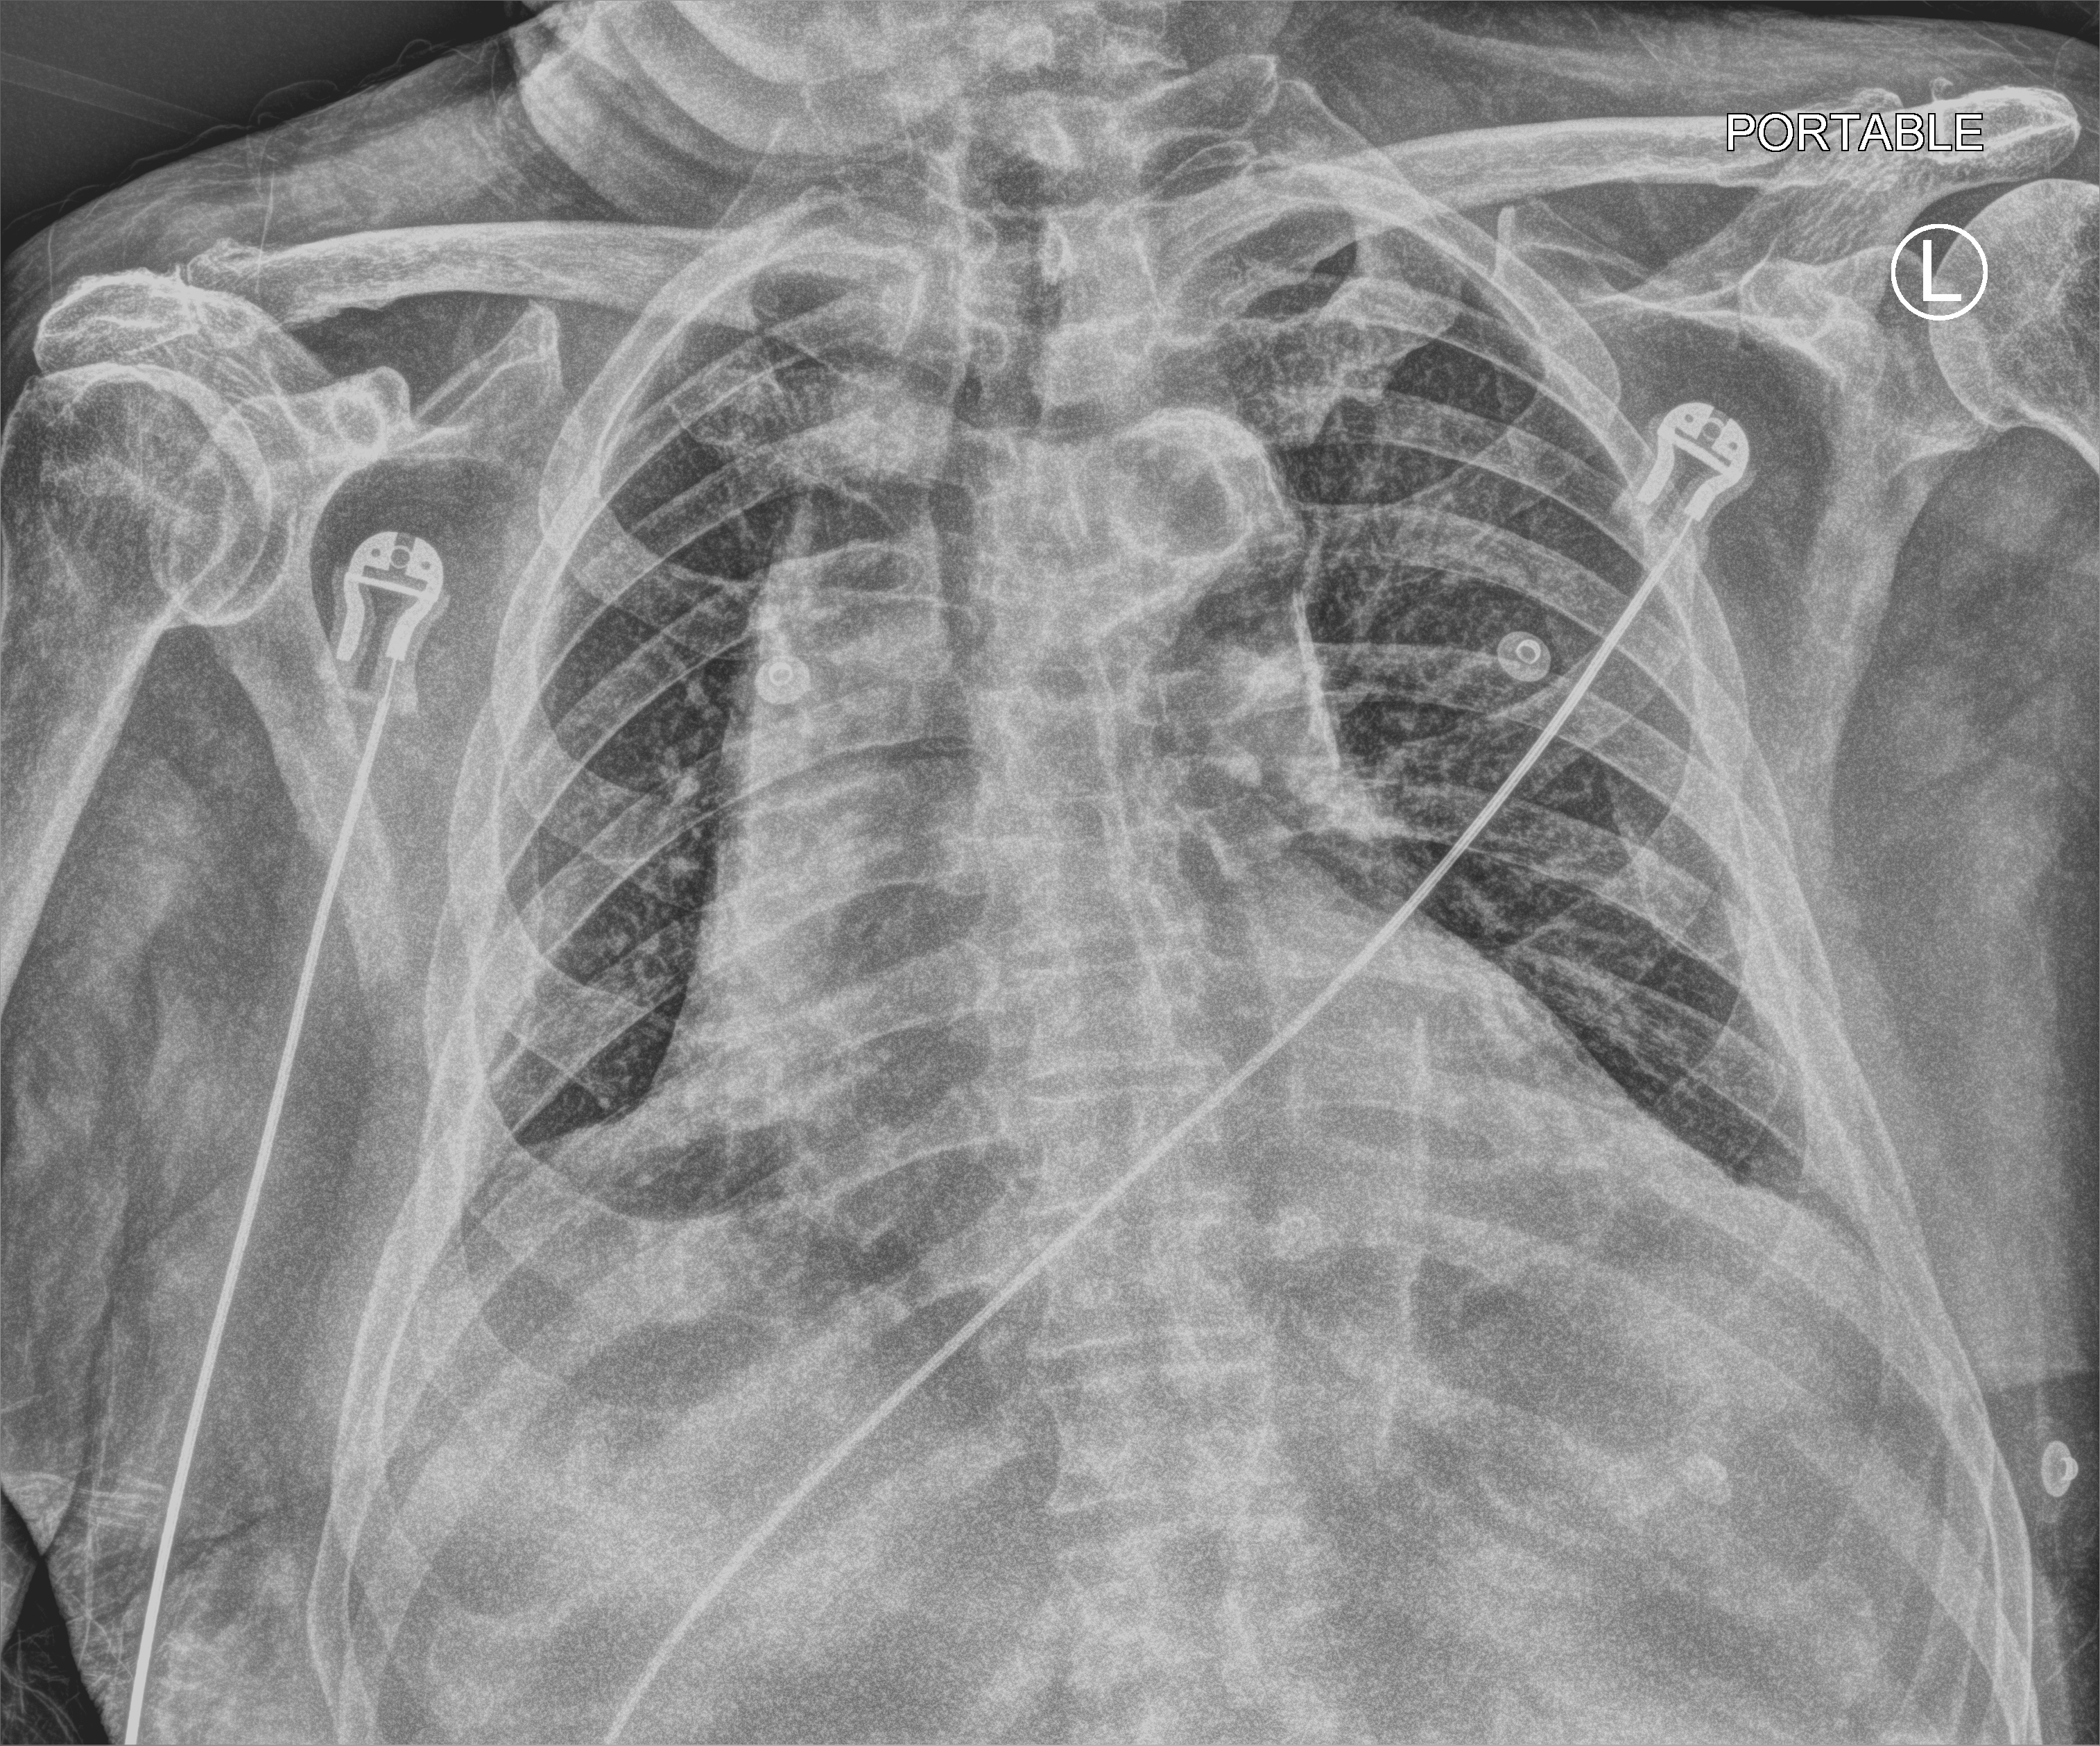
Portable chest radiograph, anteroposterior (AP) projection. Male patient hospitalised with COVID-19, age 75–90 years.
From the hospital-stay record, not from the radiograph (when in the stay this image was taken is not recorded):
- diabetes (admission record): no